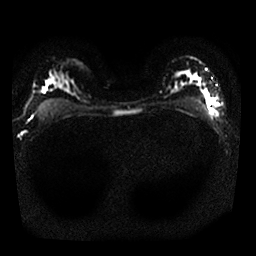
Breast MRI, one axial slice; position 18 of 25 along the scan axis; diffusion-weighted series; image 2 of 4 stored at this slice position (different b-values; order by instance number); 1.5 T; 4 mm slice thickness; 256 × 256 image matrix, field of view 320 × 320 mm. Female patient.
Annotated regions visible in this slice (outlined manually by an expert reader):
- tumour on diffusion-weighted imaging: box from (x=207, y=98) to (x=210, y=103) px